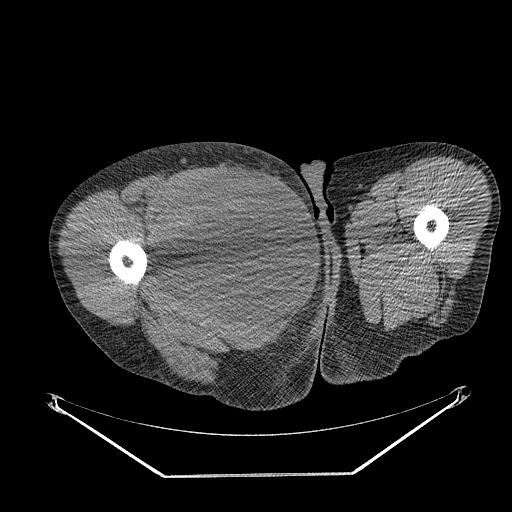
CT of an extremity soft-tissue mass (from a PET/CT study), one axial slice; slice 269 of 311 in the series (ordered by position); reconstruction kernel STANDARD; 140 kVp; soft-tissue window (W 400 / L 40 HU); 3.75 mm slice thickness; 512 × 512 image matrix. Male patient. Case-level facts recorded for this patient, not image findings: histological type: undifferentiated - pleiomorphic; grade: high; site of the primary tumour: right thigh.
Annotated regions visible in this slice (expert contour drawn on MRI and transferred to this co-registered scan by the dataset authors):
- gross tumour volume including surrounding oedema: bounding box [x1, y1, x2, y2] px = [158, 171, 268, 279]
- gross tumour volume (mass): [158, 171, 268, 279]